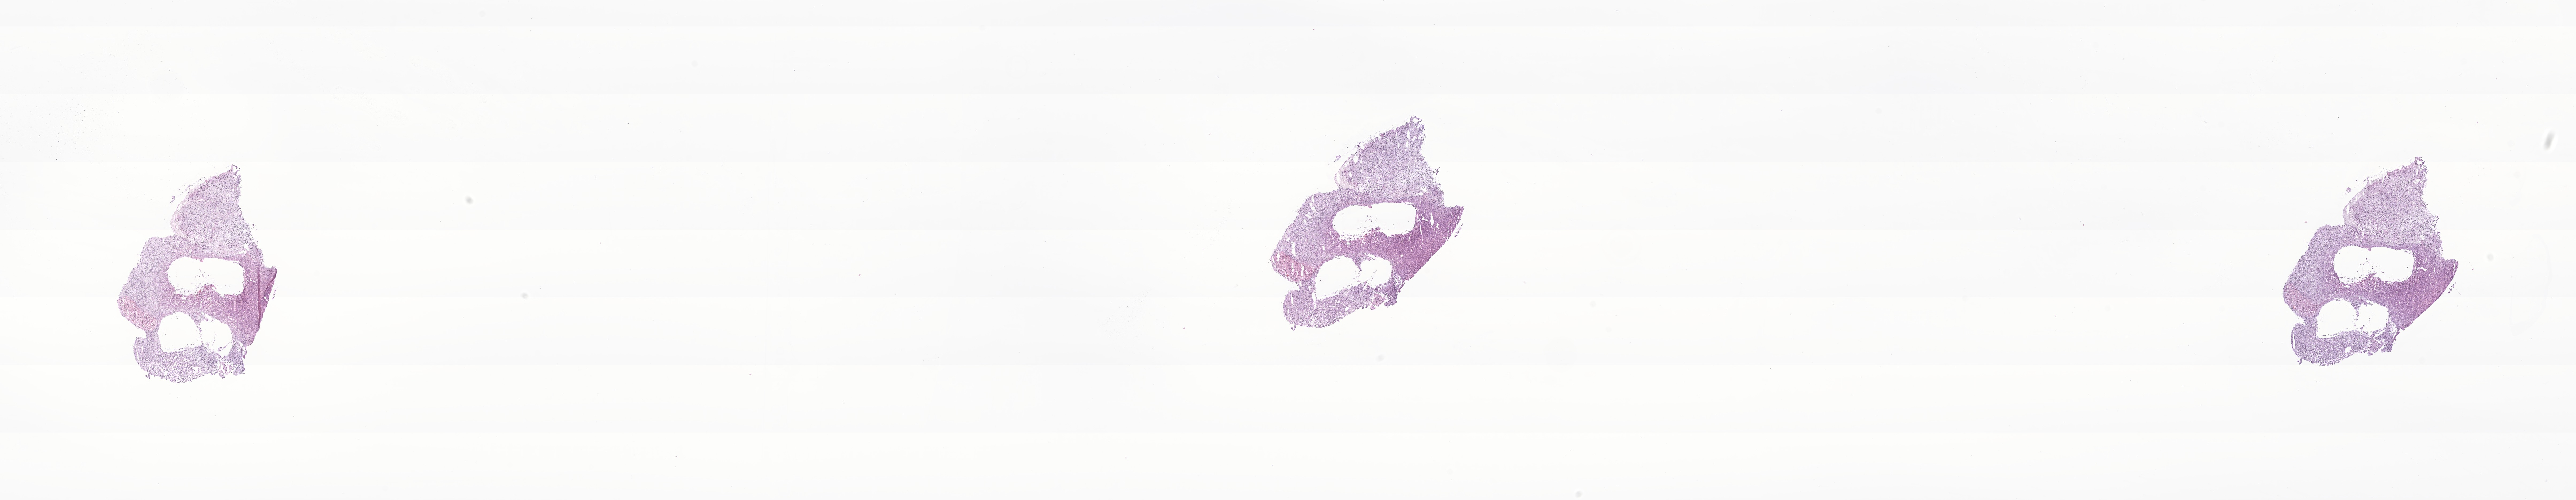
Whole-slide image, H&E stain of tumor tissue from the brain, shown as a low-resolution overview of the whole scanned area (about 40.6 x 7.9 mm); cryosection (OCT / tissue freezing medium). Patient male; age 153 months (12 years 9 months).
Recorded diagnosis: Glioma, malignant.